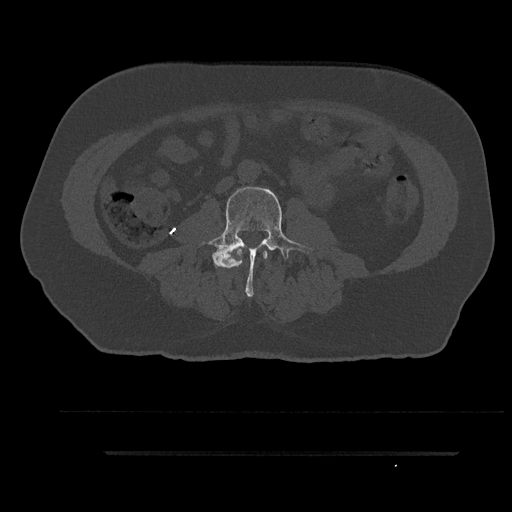
CT including the spine, one axial slice; slice 44 of 797 in the series (ordered by position); reconstruction kernel Br40s/3; 120 kVp; bone window (W 1800 / L 400 HU); 0.5 mm slice thickness; 512 × 512 image matrix. Male patient, age 63 years. Case-level facts recorded for this patient, not image findings: primary cancer: renal; vertebrae with lytic lesions (as recorded): T8.
Outlined on this slice (semi-automatically segmented with operator editing):
- L2 vertebra: box from (x=235, y=248) to (x=268, y=266) px
- L3 vertebra: (x=199, y=185)–(x=314, y=297)